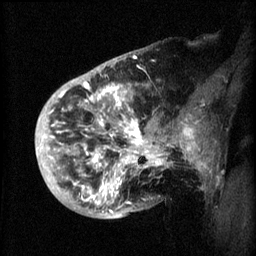
Breast MRI (dynamic contrast-enhanced), one sagittal slice; slice 15 of 60 in the series (ordered by position); 3 images stored at this slice position (order not interpretable as contrast timing); 1.5 T; TE 4.2 ms, TR 8.2 ms; 2 mm slice thickness; 256 × 256 image matrix. Female patient, age 50 years.
Annotated regions visible in this slice (semi-automatic segmentation, software-assisted and operator-edited):
- analysis volume of interest (the breast-tissue region the enhancement analysis was run in; not a lesion): bounding box <44,72,173,219> (left, top, right, bottom; pixels)
- tumour enhancement mask (voxels above the 70 % enhancement threshold inside the analysis volume of interest): <53,82,166,215>